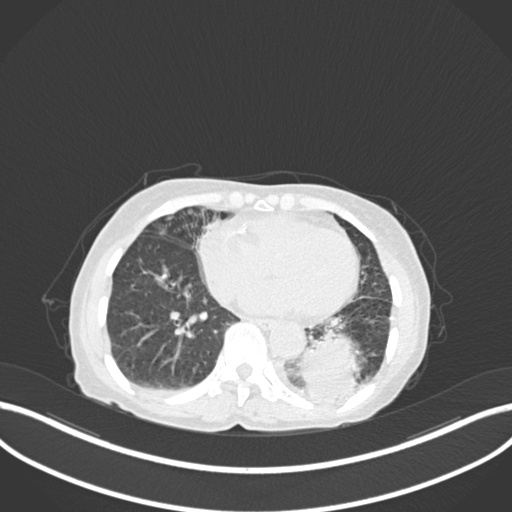
Chest CT, one axial slice. Position 41 of 233 along the scan axis. Reconstruction kernel B30f. 120 kVp. Lung window (W 1500 / L -600 HU). 1 mm slice thickness. 512 × 512 image matrix, field of view 400 × 400 mm. Patient: female, 78 years. Case-level facts recorded for this patient, not image findings: clinical TNM (as recorded): T3 N0 M1.
Outlined on this slice (rectangle marked by the reading radiologist):
- lung tumour (recorded histology: squamous cell carcinoma): bounding box [x1, y1, x2, y2] px = [298, 328, 359, 389]